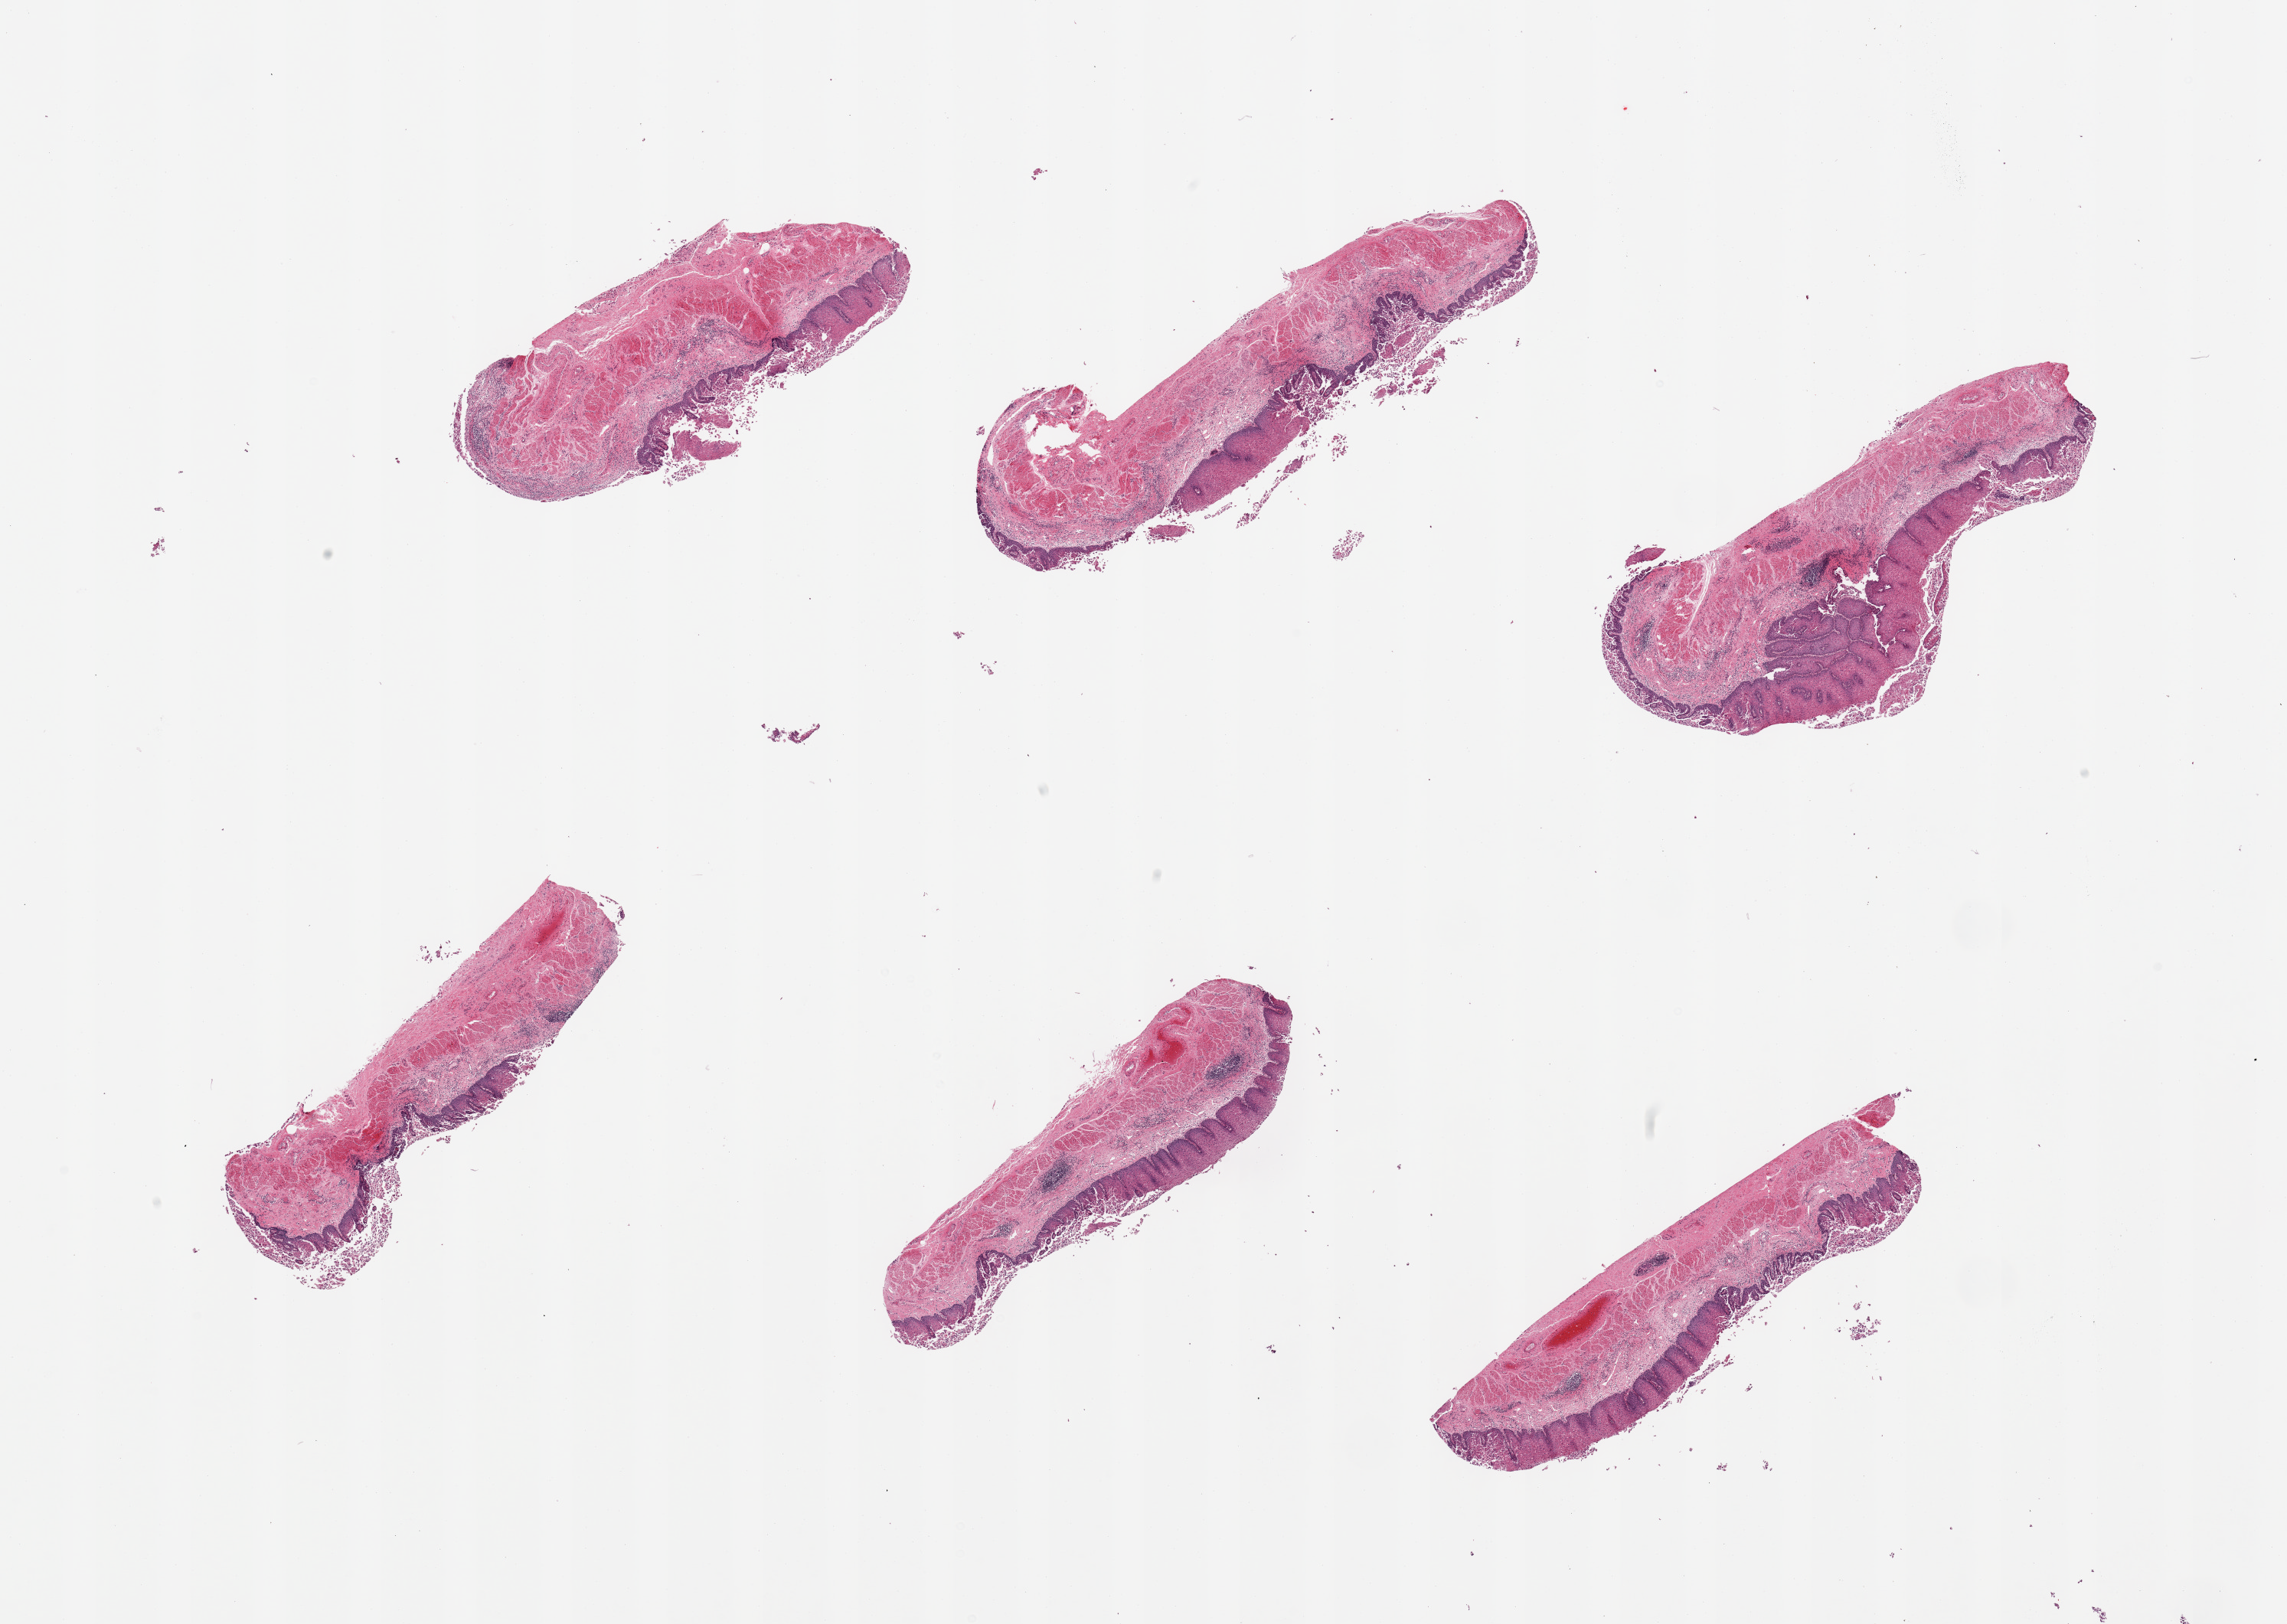
Hematoxylin and eosin (H&E) whole-slide image, a low-resolution overview of the entire scanned area, about 23.6 x 16.8 mm. PAXgene-fixed paraffin-embedded (PFPE) section. Section of esophageal mucous membrane (target tissue). Tissue donor sample. Female donor.
• review note (as recorded): 6 pieces; chronically inflammed, epithelium sloughing